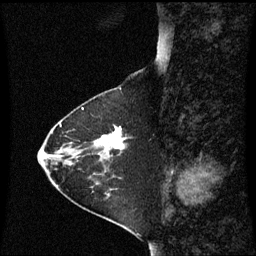
Breast MRI (dynamic contrast-enhanced), one sagittal slice; slice 21 of 60 in the series (ordered by position); dynamic contrast-enhanced series, image 2 of 3 at this slice position (ordered by acquisition); 1.5 T; TE 4.2 ms, TR 8.9 ms; 2 mm slice thickness; 256 × 256 image matrix, field of view 210 × 210 mm. Female patient, age 63 years. From the clinical record (not read from this slice): setting: breast cancer imaged before/during neoadjuvant chemotherapy; receptor status: HR-positive, HER2-negative.
Annotated regions visible in this slice (semi-automatic segmentation, software-assisted and operator-edited):
- analysis volume of interest (the breast-tissue region the enhancement analysis was run in; not a lesion): box from (x=88, y=127) to (x=126, y=163) px
- tumour enhancement mask (voxels above the 70 % enhancement threshold inside the analysis volume of interest): (x=99, y=128)–(x=125, y=150)